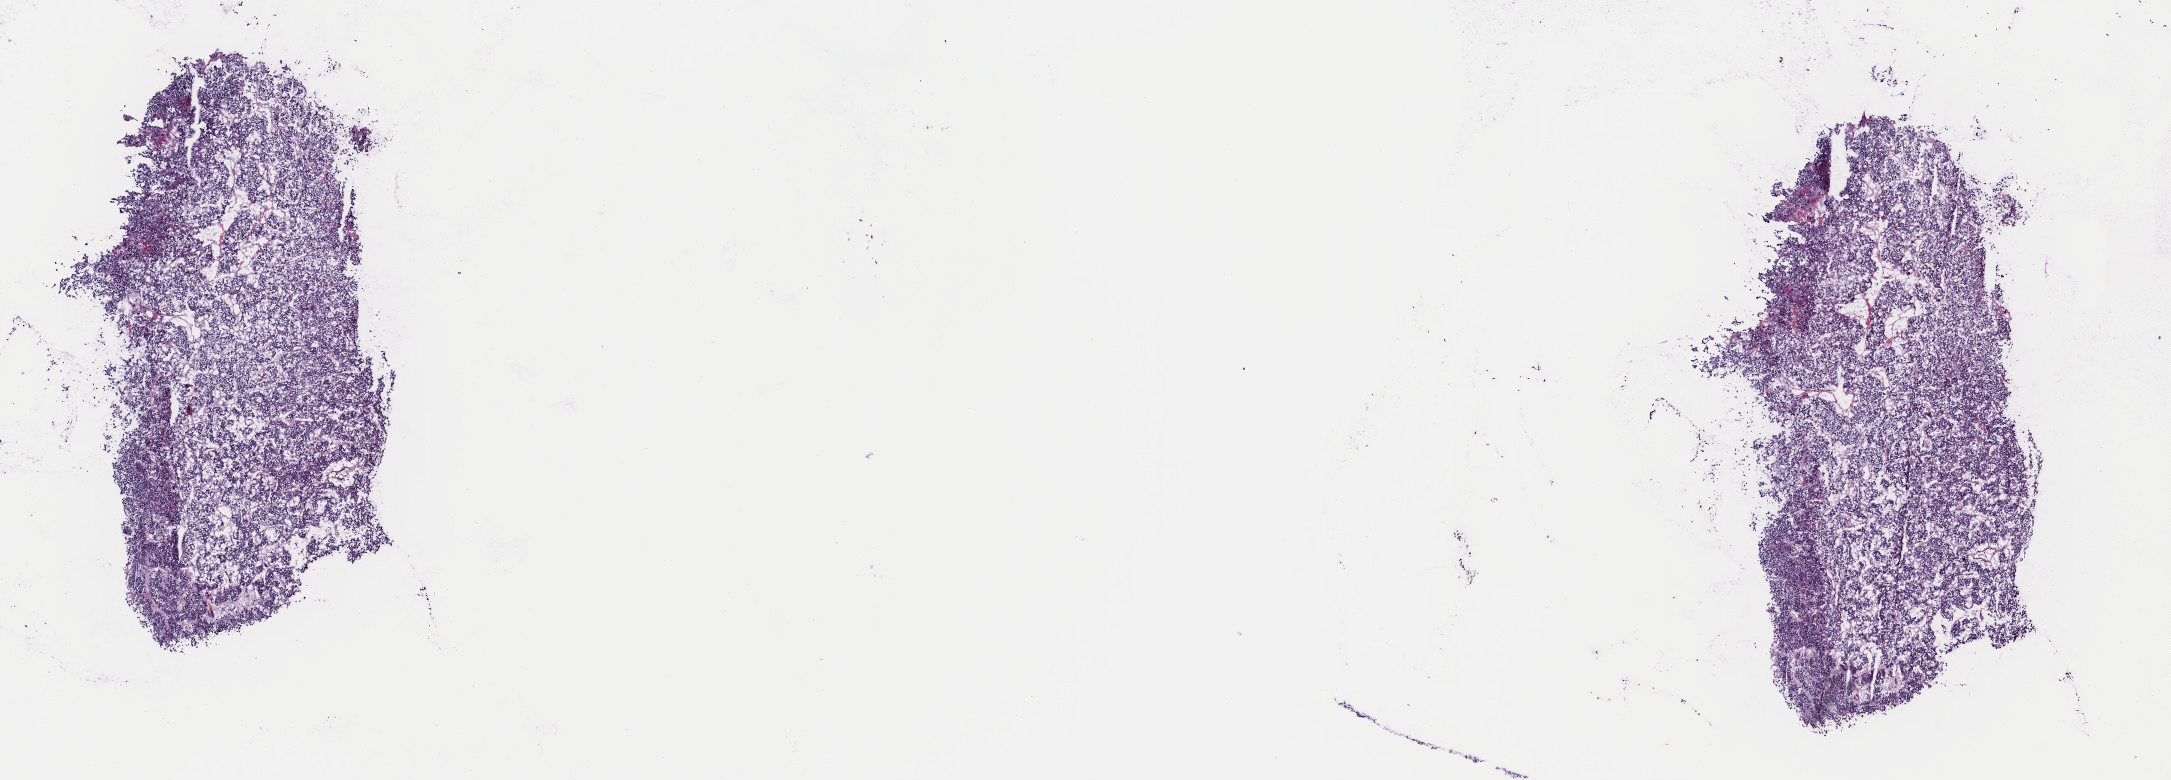
H&E-stained whole-slide image — shown as a low-resolution overview of the whole scanned area (about 17.2 x 6.2 mm), frozen section, primary tumour sample from the adrenal gland. Female patient; age at initial diagnosis 57 years. Pathologist review of this section (percent, as recorded): tumour cells 100%, tumour nuclei 80%, normal cells 0%, stromal cells 0%, necrosis 0%. Inflammatory infiltration, as recorded: lymphocyte infiltration 1%, monocyte infiltration 0%, neutrophil infiltration 0%.
Diagnosis: Pheochromocytoma, NOS (cortex of adrenal gland).